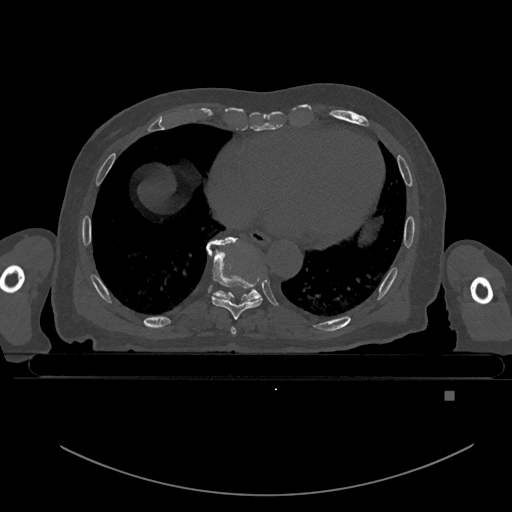
CT including the spine, one axial slice. Slice 186 of 969 in the series (ordered by position). Bone window (W 1800 / L 400 HU). 0.5 mm slice thickness. 512 × 512 image matrix, field of view 456 × 456 mm. Patient: male, 82 years. Case-level facts recorded for this patient, not image findings: primary cancer: prostate.
Structures marked on this image (semi-automatic segmentation, software-assisted and operator-edited):
- T7 vertebra: bounding box (x1, y1, x2, y2) in pixels: (231, 326, 236, 335)
- T8 vertebra: (209, 240, 263, 320)
- T9 vertebra: (206, 236, 261, 302)